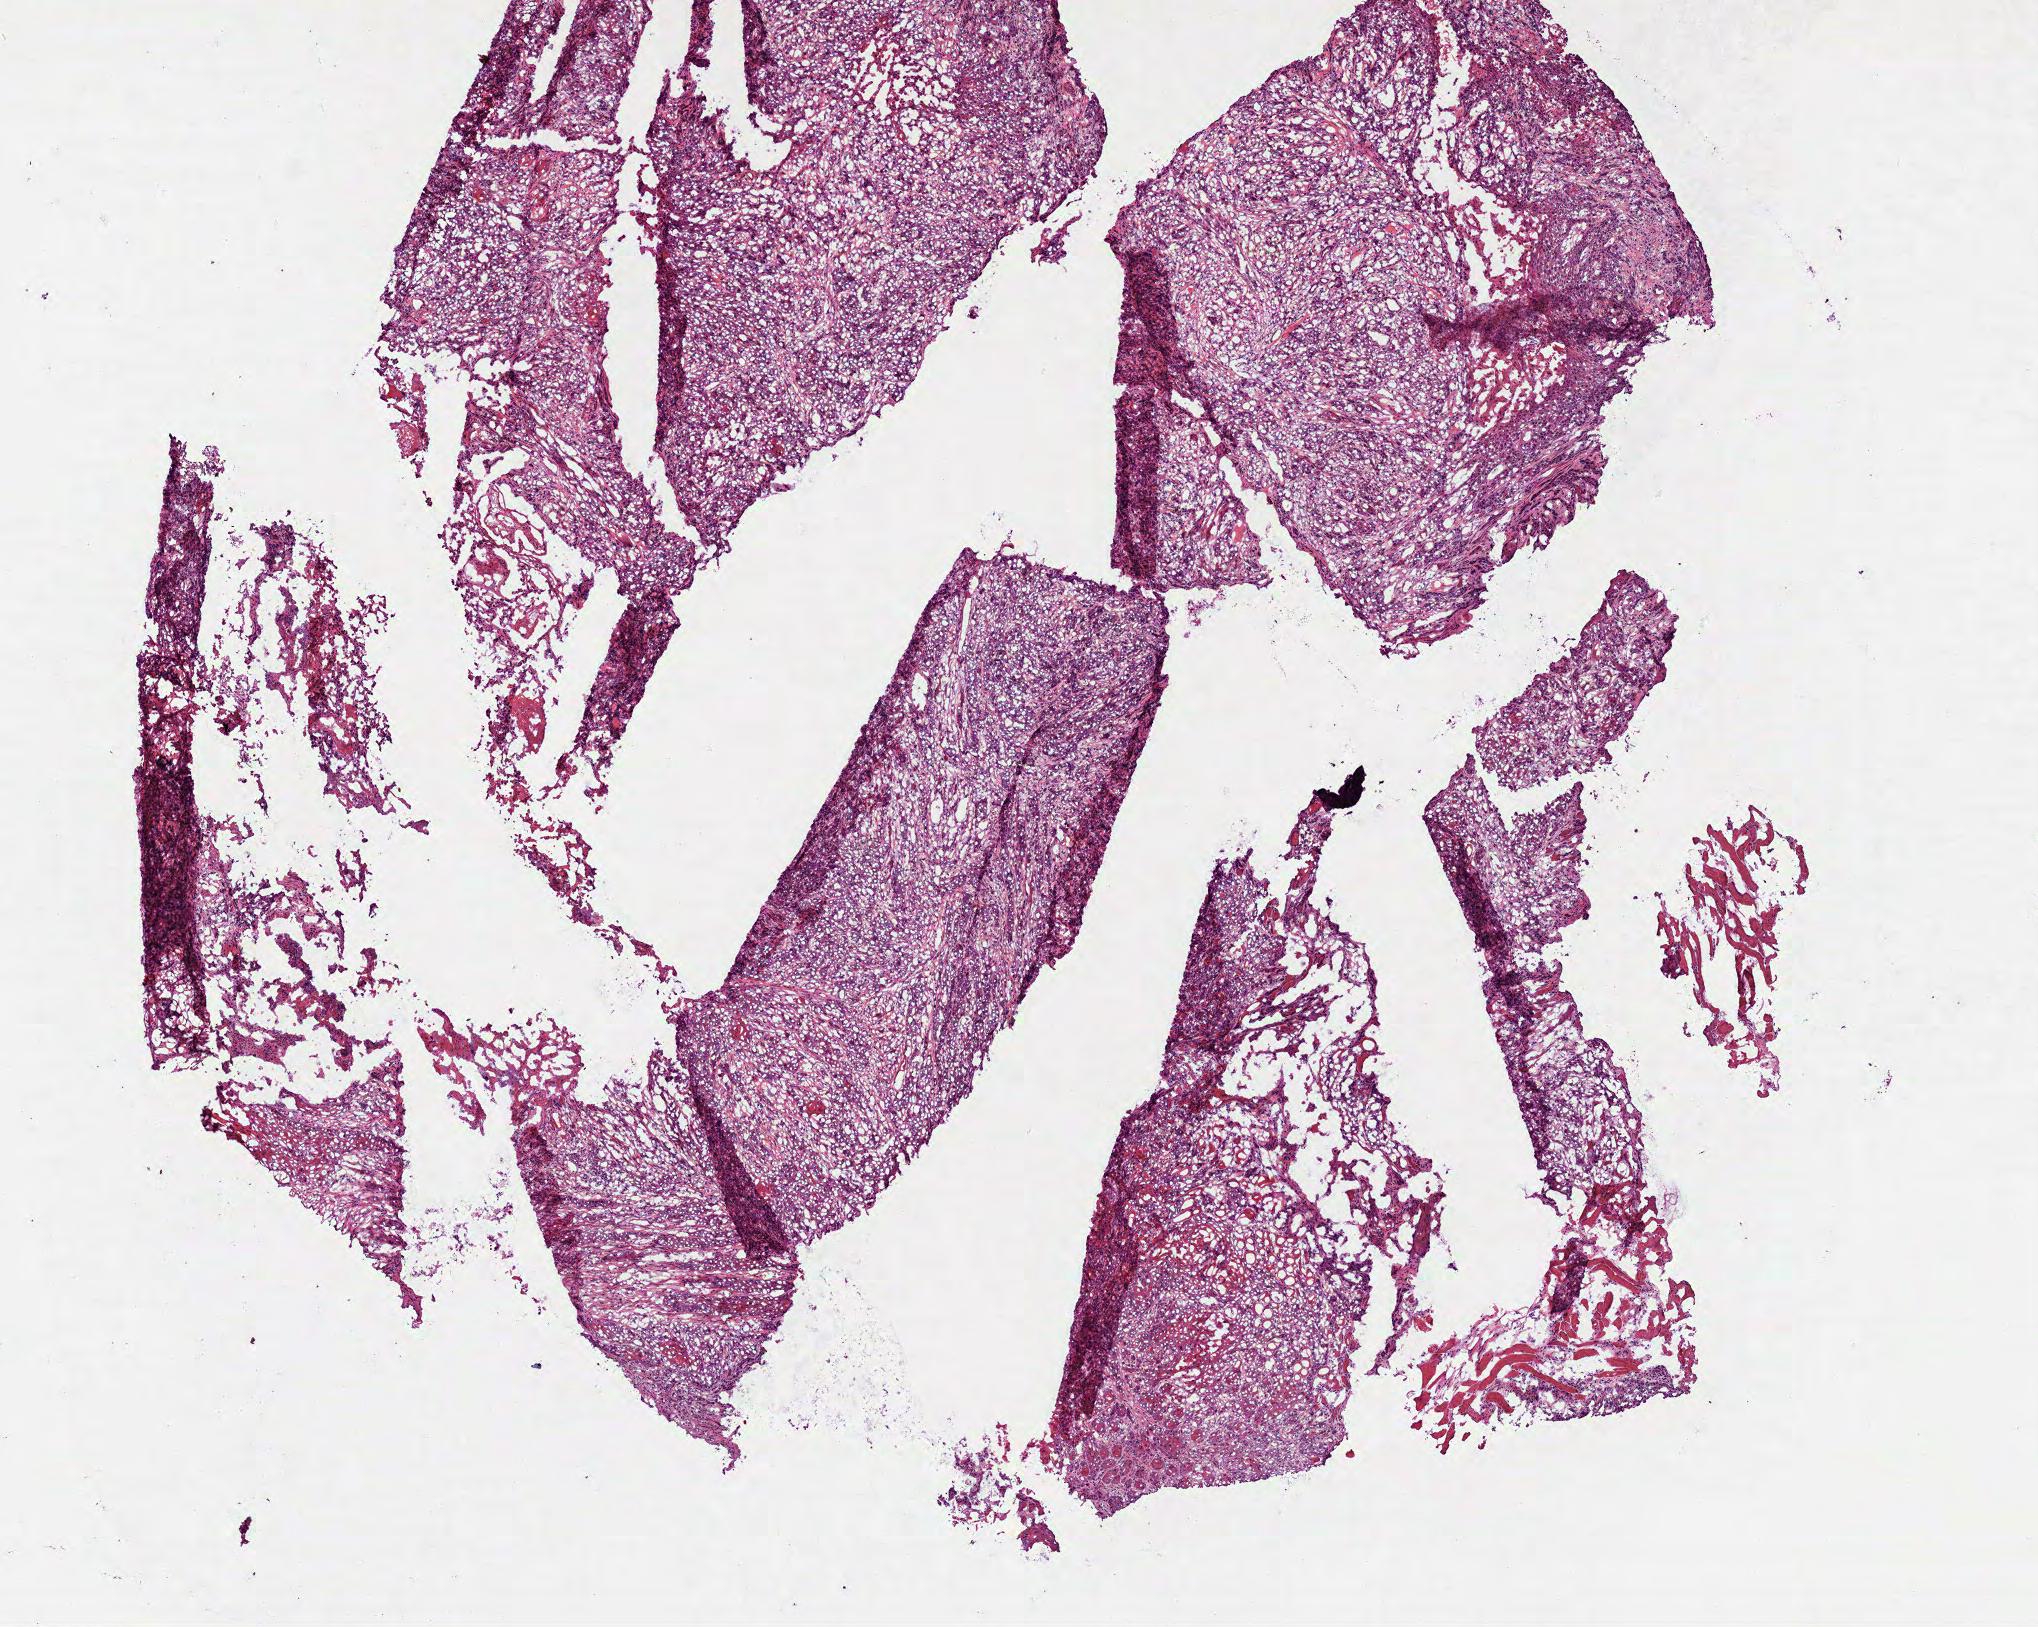
Whole-slide histology image, H&E-stained, a low-resolution overview of the entire scanned area, about 8.2 x 6.6 mm. Frozen section from the top of the tissue portion. Sample: primary tumour, head and neck. Patient: male, age at initial diagnosis 64 years. Histologic grade: G2 (moderately differentiated). Slide review estimates, as recorded: tumour cells 99%, tumour nuclei 90%, normal cells 0%, stromal cells 0%, necrosis 1%. Infiltration values recorded for this section: lymphocyte infiltration 0%, monocyte infiltration 0%, neutrophil infiltration 0%.
- diagnosis: Squamous cell carcinoma, NOS
- AJCC pathologic stage: IVA (7th edition)